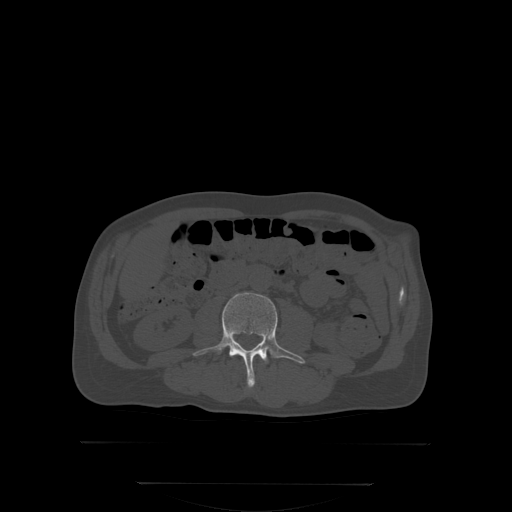
CT including the spine, one axial slice. Slice 123 of 350 in the series (ordered by position). Bone window (W 1800 / L 400 HU). 2.5 mm slice thickness. 512 × 512 image matrix, field of view 500 × 500 mm. Patient: male, 58 years. Case-level facts recorded for this patient, not image findings: primary cancer: prostate; vertebrae with lytic lesions (as recorded): L1.
Structures marked on this image (semi-automatic segmentation, software-assisted and operator-edited):
- L3 vertebra: bounding box (x1, y1, x2, y2) in pixels: (193, 292, 306, 388)